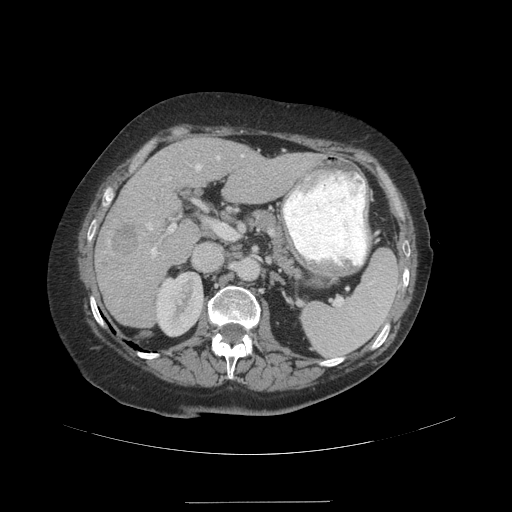
Contrast-enhanced abdominal CT (liver protocol), one axial slice. 140 kVp. Soft-tissue window (W 400 / L 40 HU). 512 × 512 image matrix, field of view 440 × 440 mm. Case-level facts recorded for this patient, not image findings: diagnosis: hepatocellular carcinoma (patient treated with transarterial chemoembolisation; whether this scan precedes or follows treatment is not stated here); TNM stage (as recorded): Stage-IVA; Child-Pugh class: A; tumour nodularity: multinodular.
Outlined on this slice (semi-automatic segmentation, software-assisted and operator-edited):
- liver parenchyma outside the tumour (the mass and vessels are separate outlines, so this box may not span the whole liver): bounding box [x1, y1, x2, y2] px = [94, 136, 320, 328]
- mass: [112, 224, 139, 256]
- liver vessels: [108, 155, 244, 258]